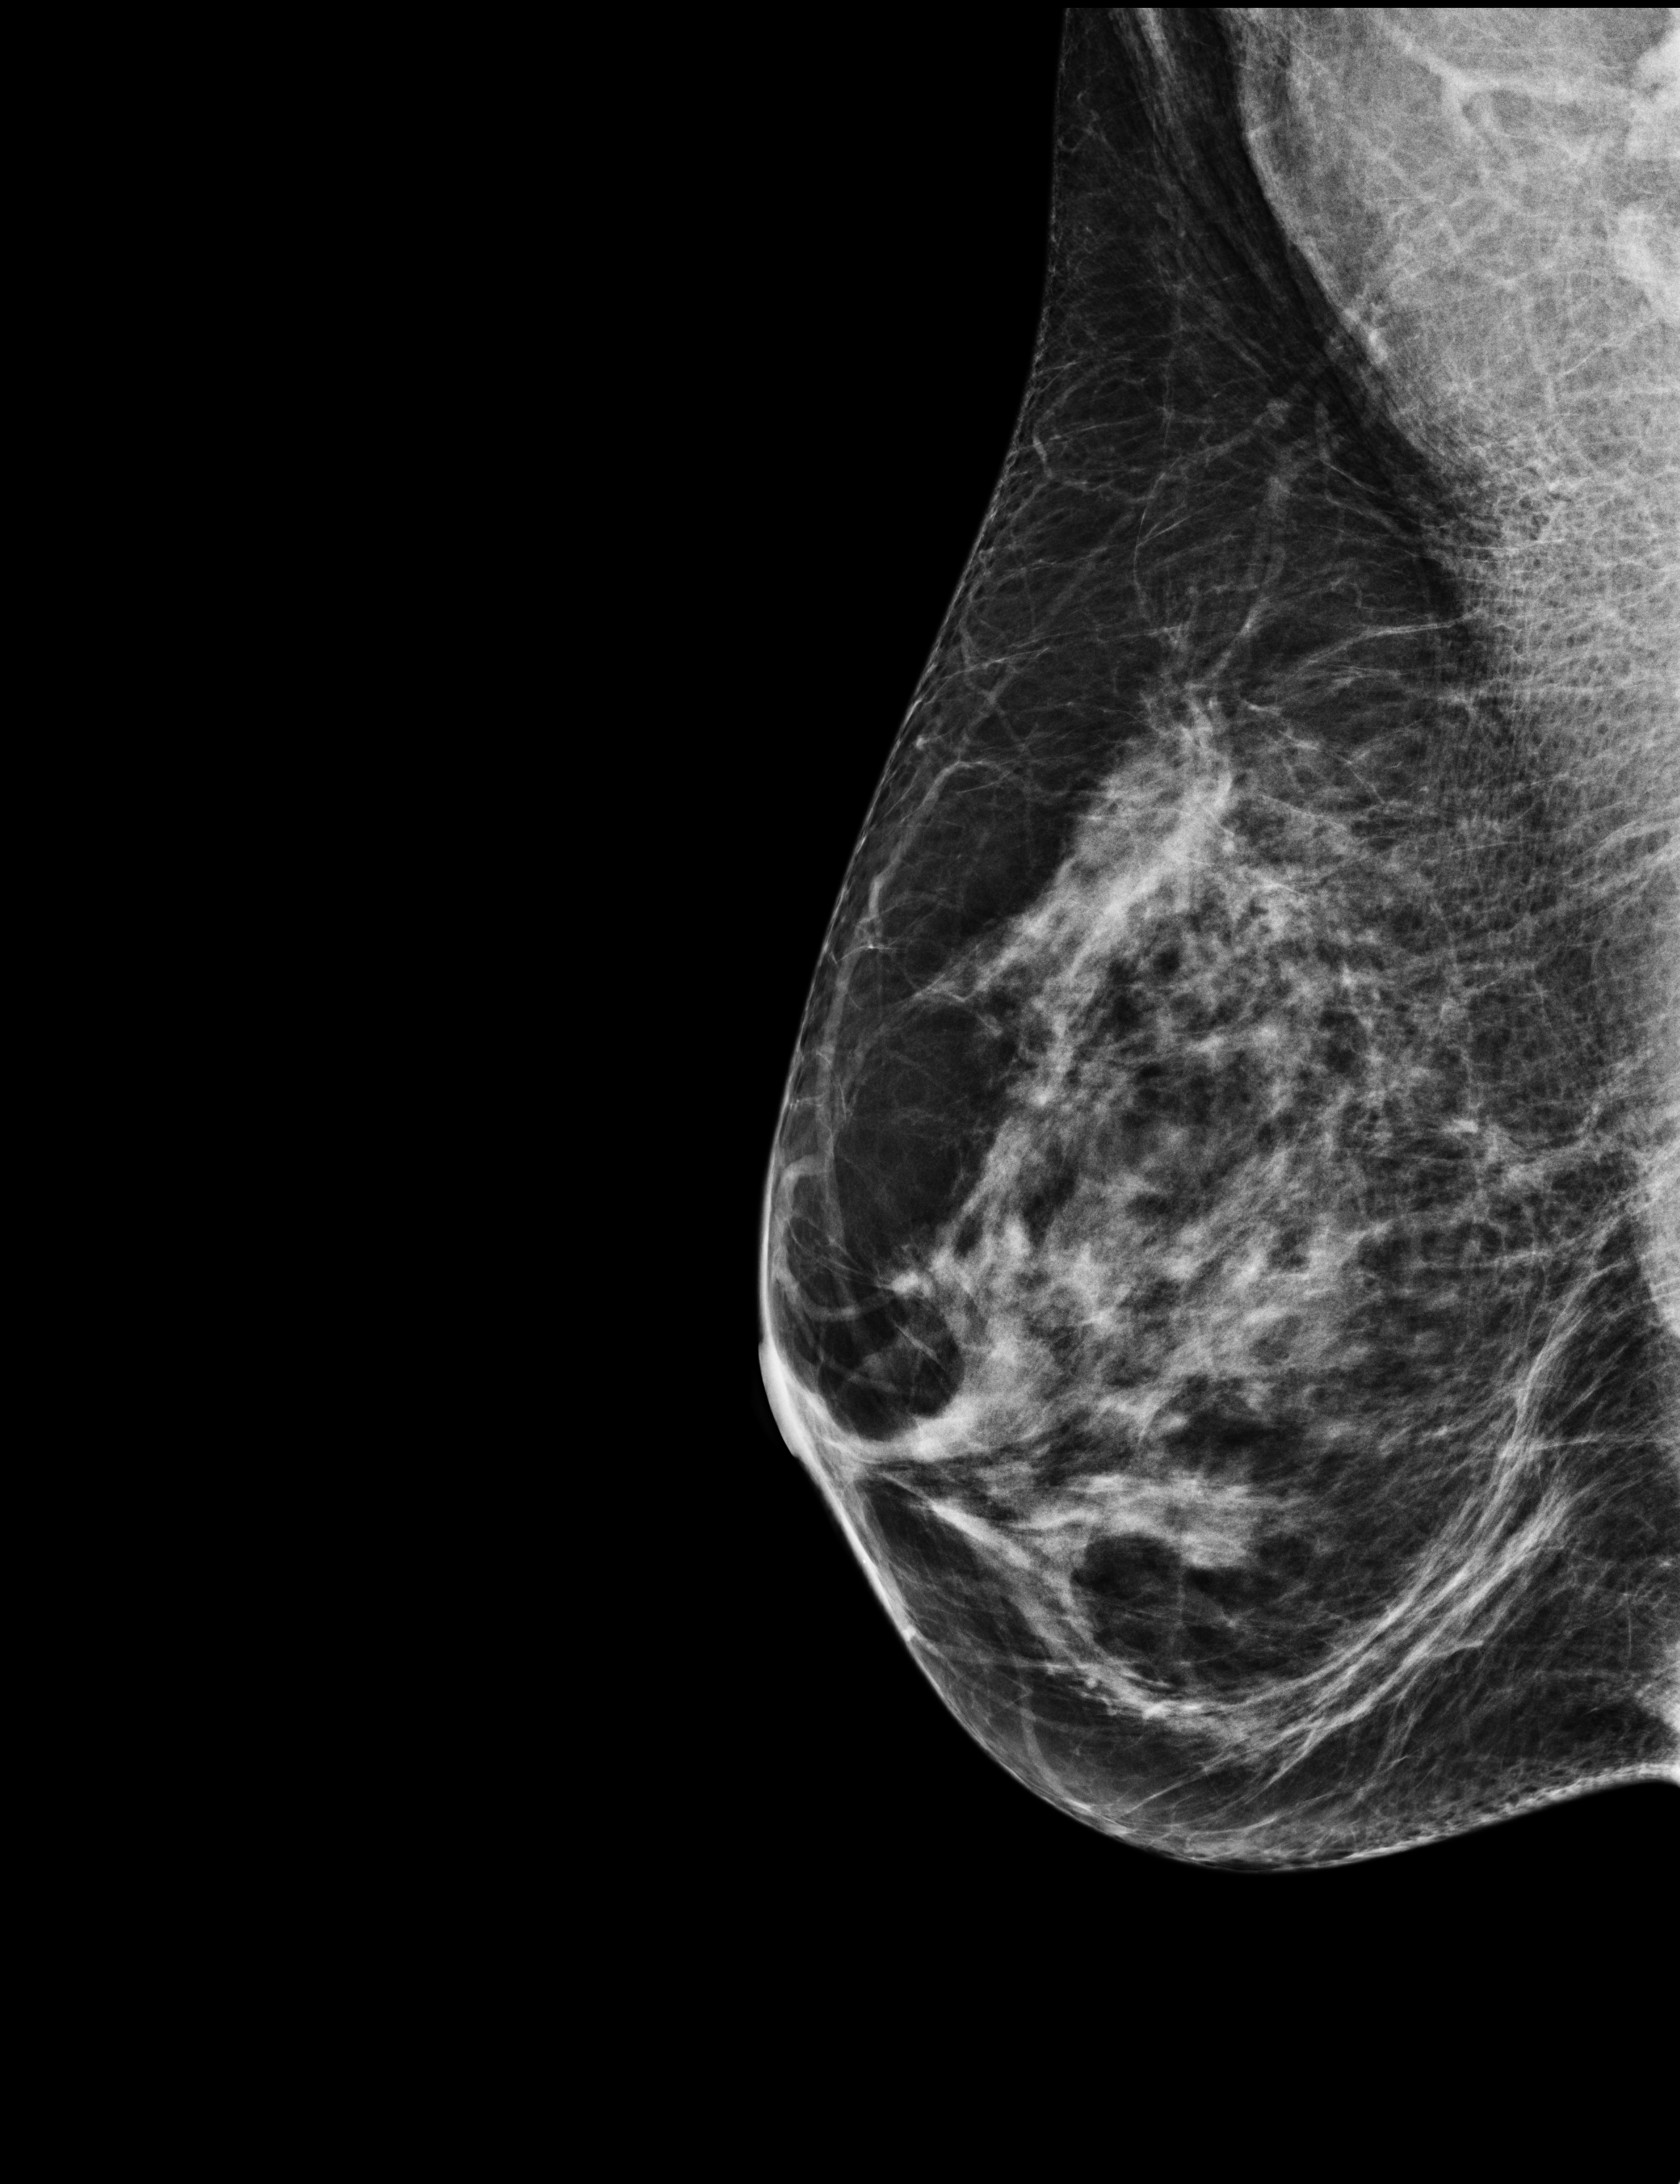
Full-field digital mammogram (FFDM), right breast, medio-lateral oblique projection, annual screening mammography examination, system: Selenia Dimensions. Patient aged 56 years (female).
Final BI-RADS assessment for this screening round (tomosynthesis exam, both breasts): category 1.